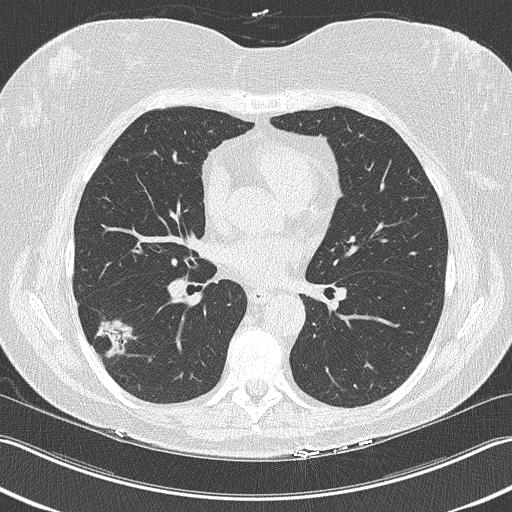
Low-dose screening chest CT, one axial slice; slice 116 of 210 in the series (ordered by position); reconstruction kernel B50f; lung window (W 1500 / L -600 HU); 512 × 512 image matrix, field of view 348 × 348 mm.
Outlined on this slice (expert manual segmentation):
- lesion 1 (tumor, lower lobe of right lung): bounding box <95,318,138,358> (left, top, right, bottom; pixels)